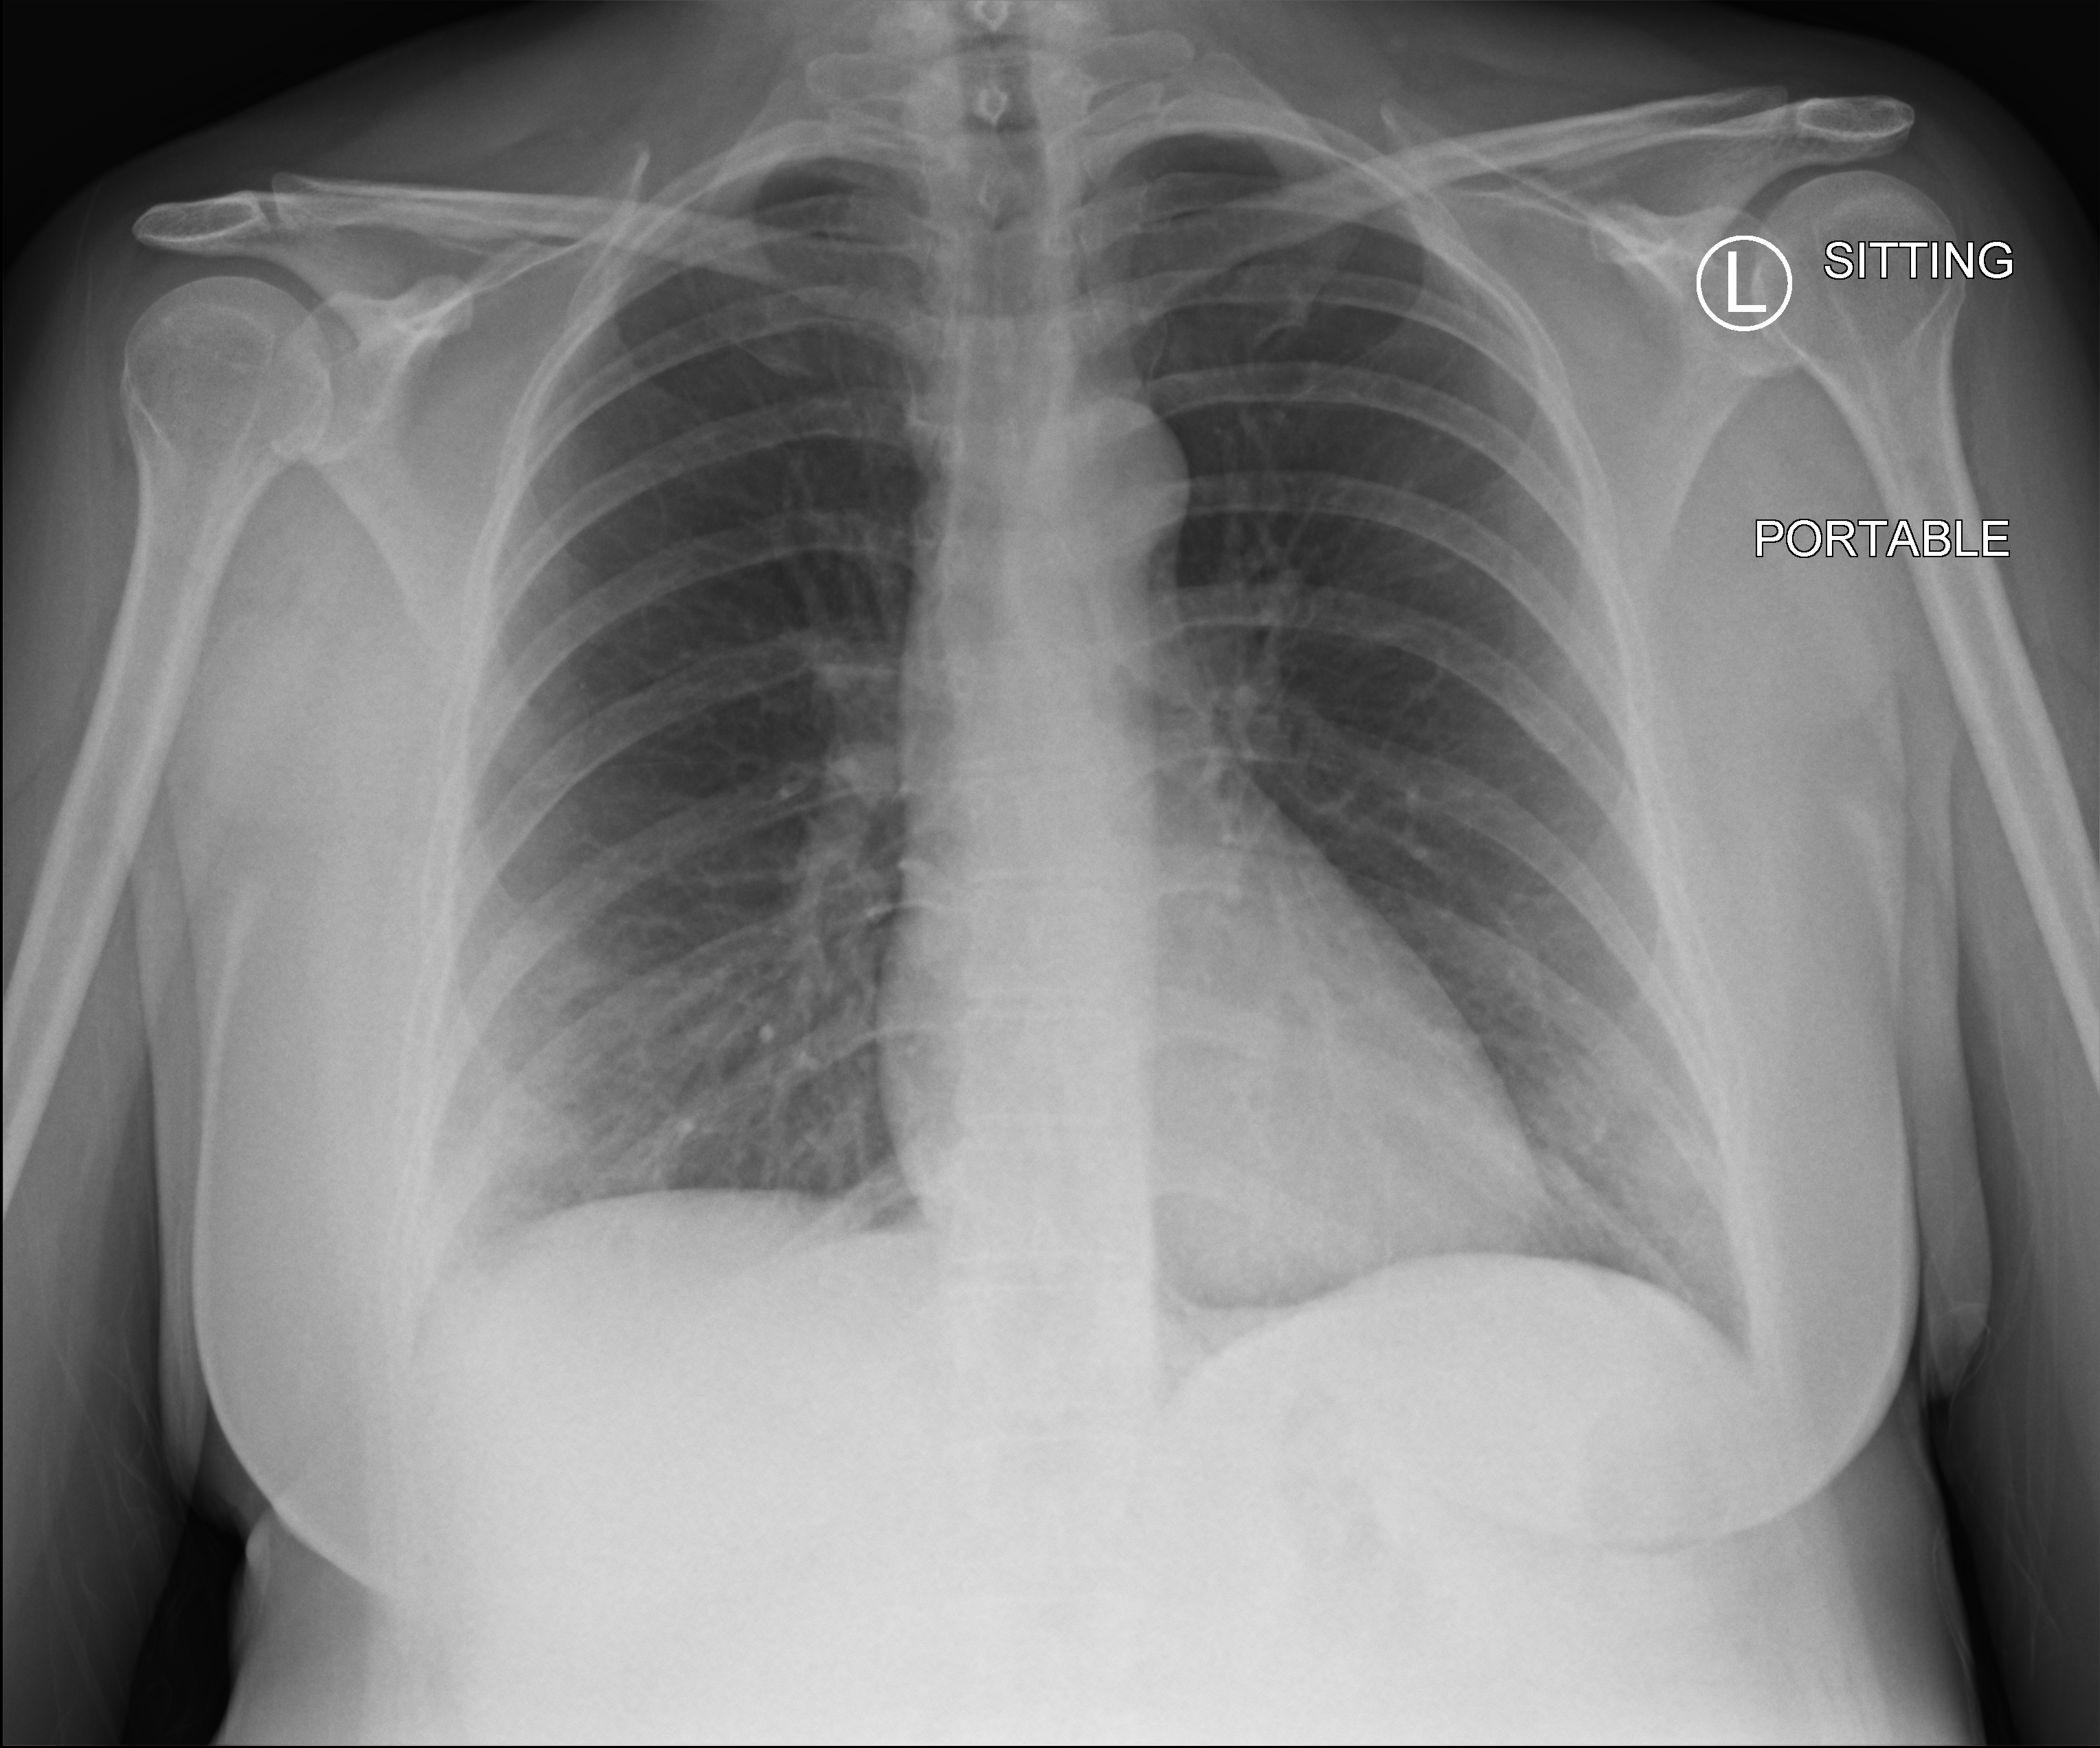
Bedside chest radiograph (computed radiography), anteroposterior (AP) projection. Female patient hospitalised with COVID-19, age 18–59 years.
Hospital-stay facts (about this admission, not read from this image; timing relative to this image not recorded):
- mechanically ventilated during this hospital stay: no
- admitted to intensive care during this hospital stay: no